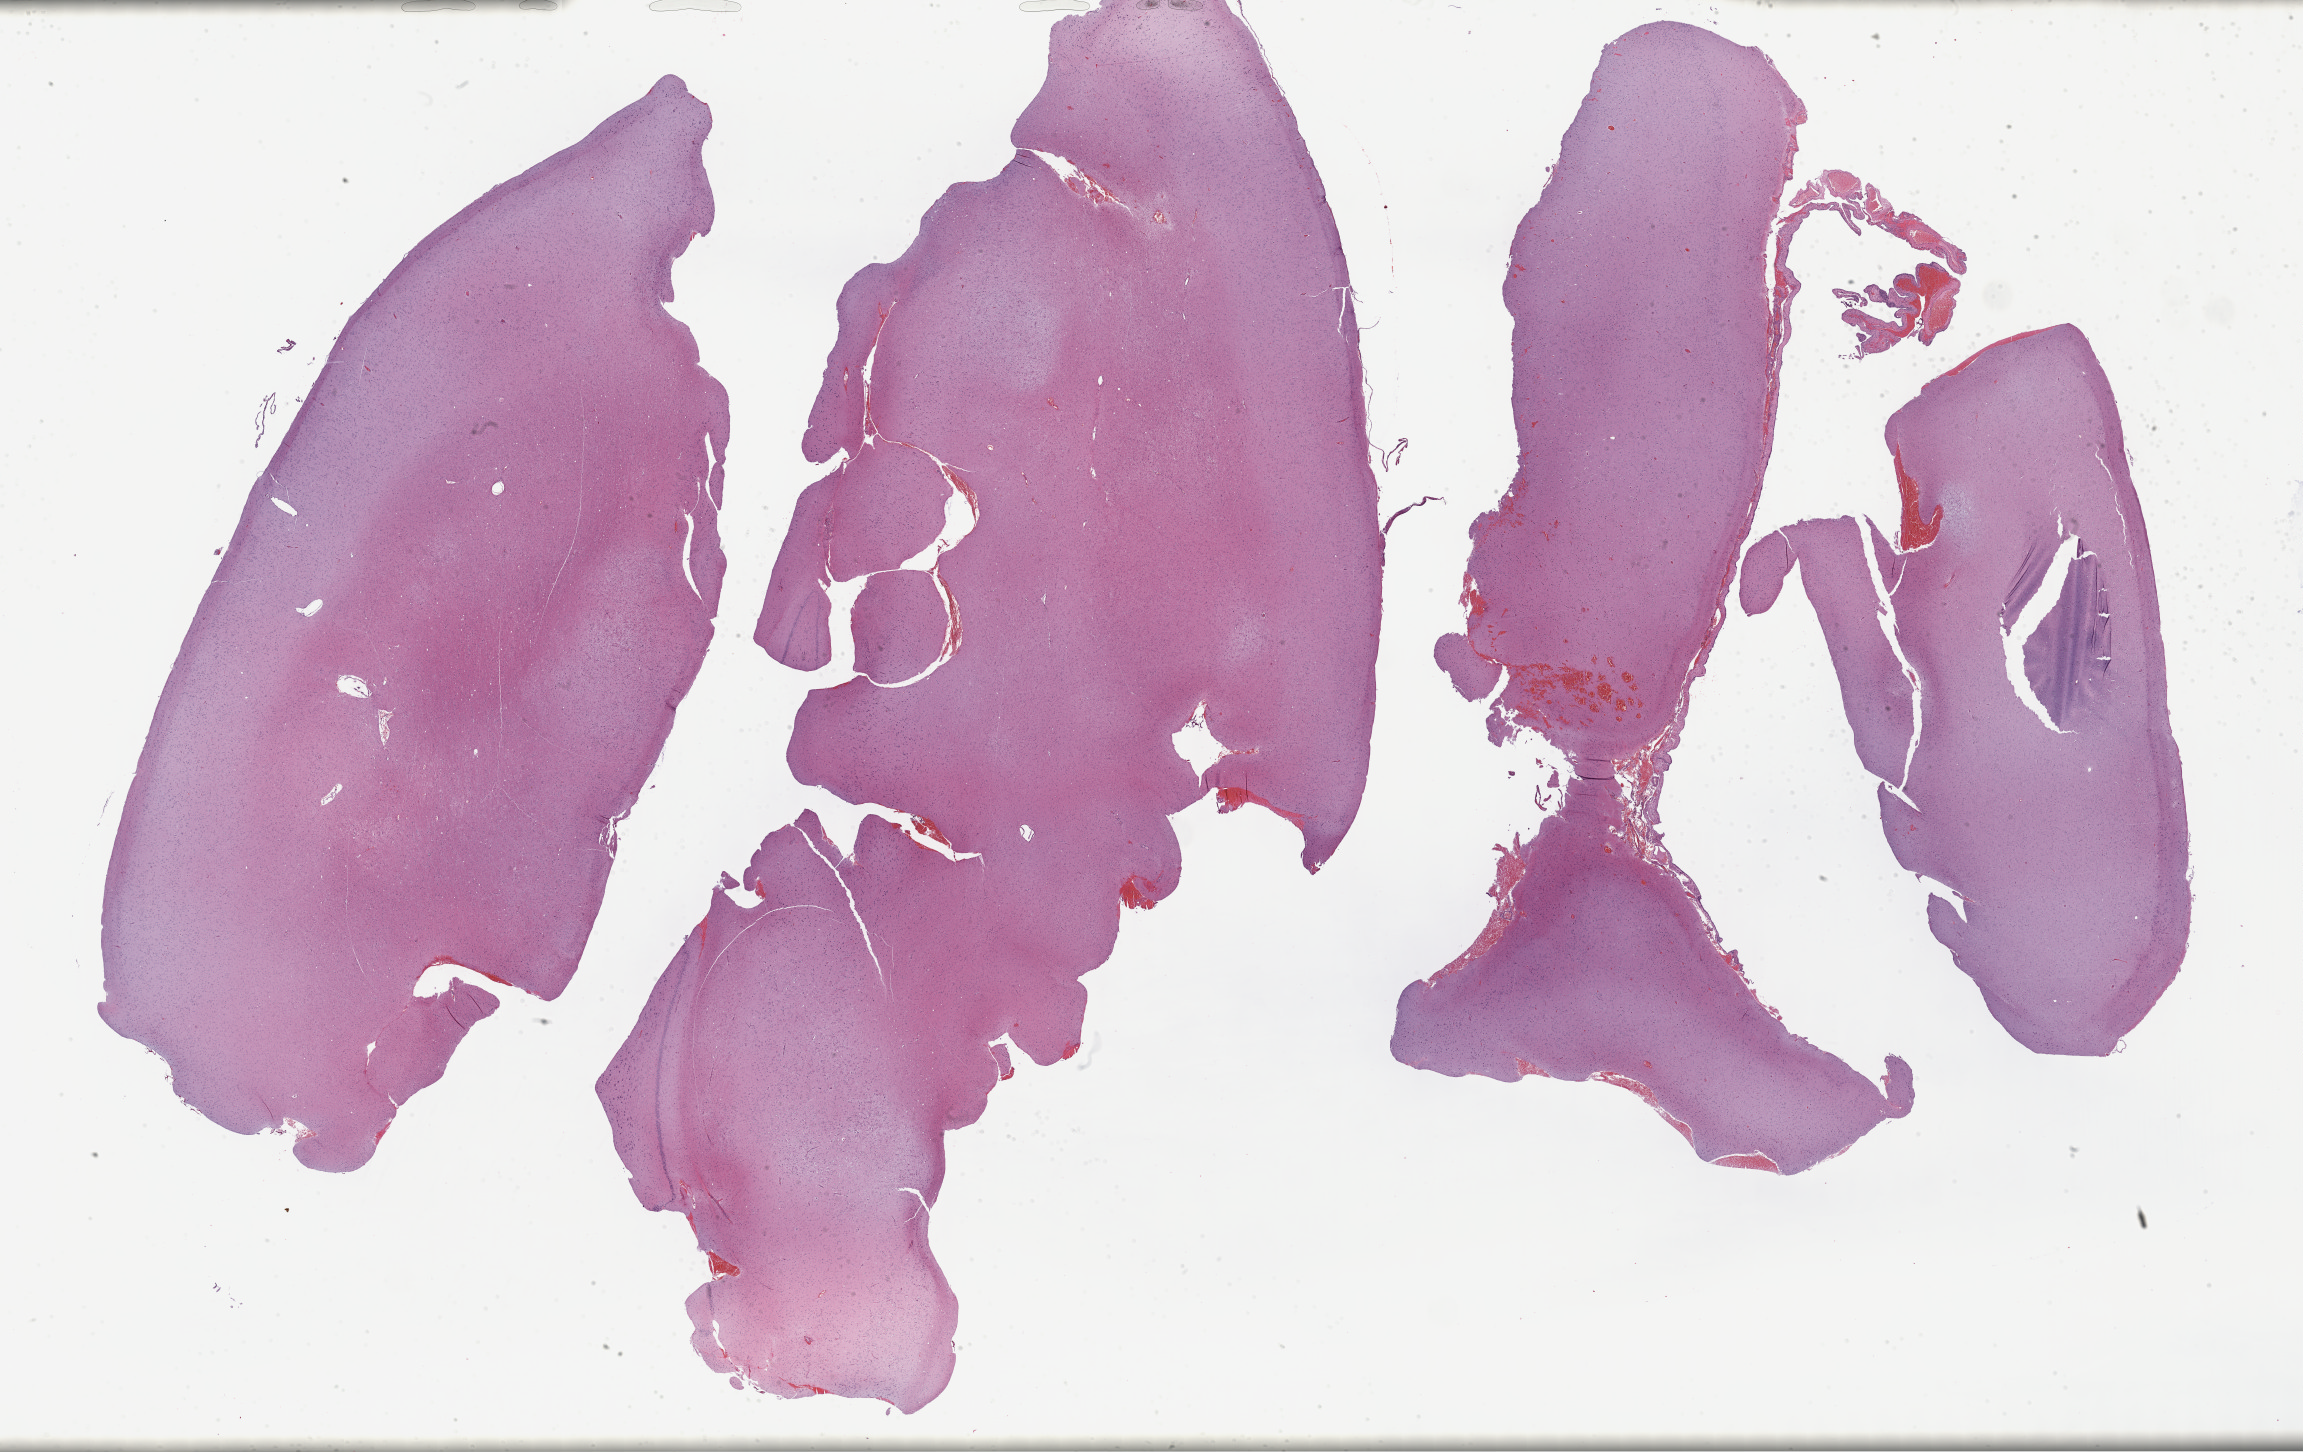
Hematoxylin and eosin (H&E) stained whole-slide image, low-resolution overview of the scanned area, about 37.2 x 23.5 mm (slide scanned at 40x); formalin-fixed paraffin-embedded (FFPE) diagnostic section; brain, primary tumour sample. Patient: female, age at initial diagnosis 37 years. Histologic grade: G2 (moderately differentiated).
Histologic diagnosis: Astrocytoma, NOS (cerebrum).